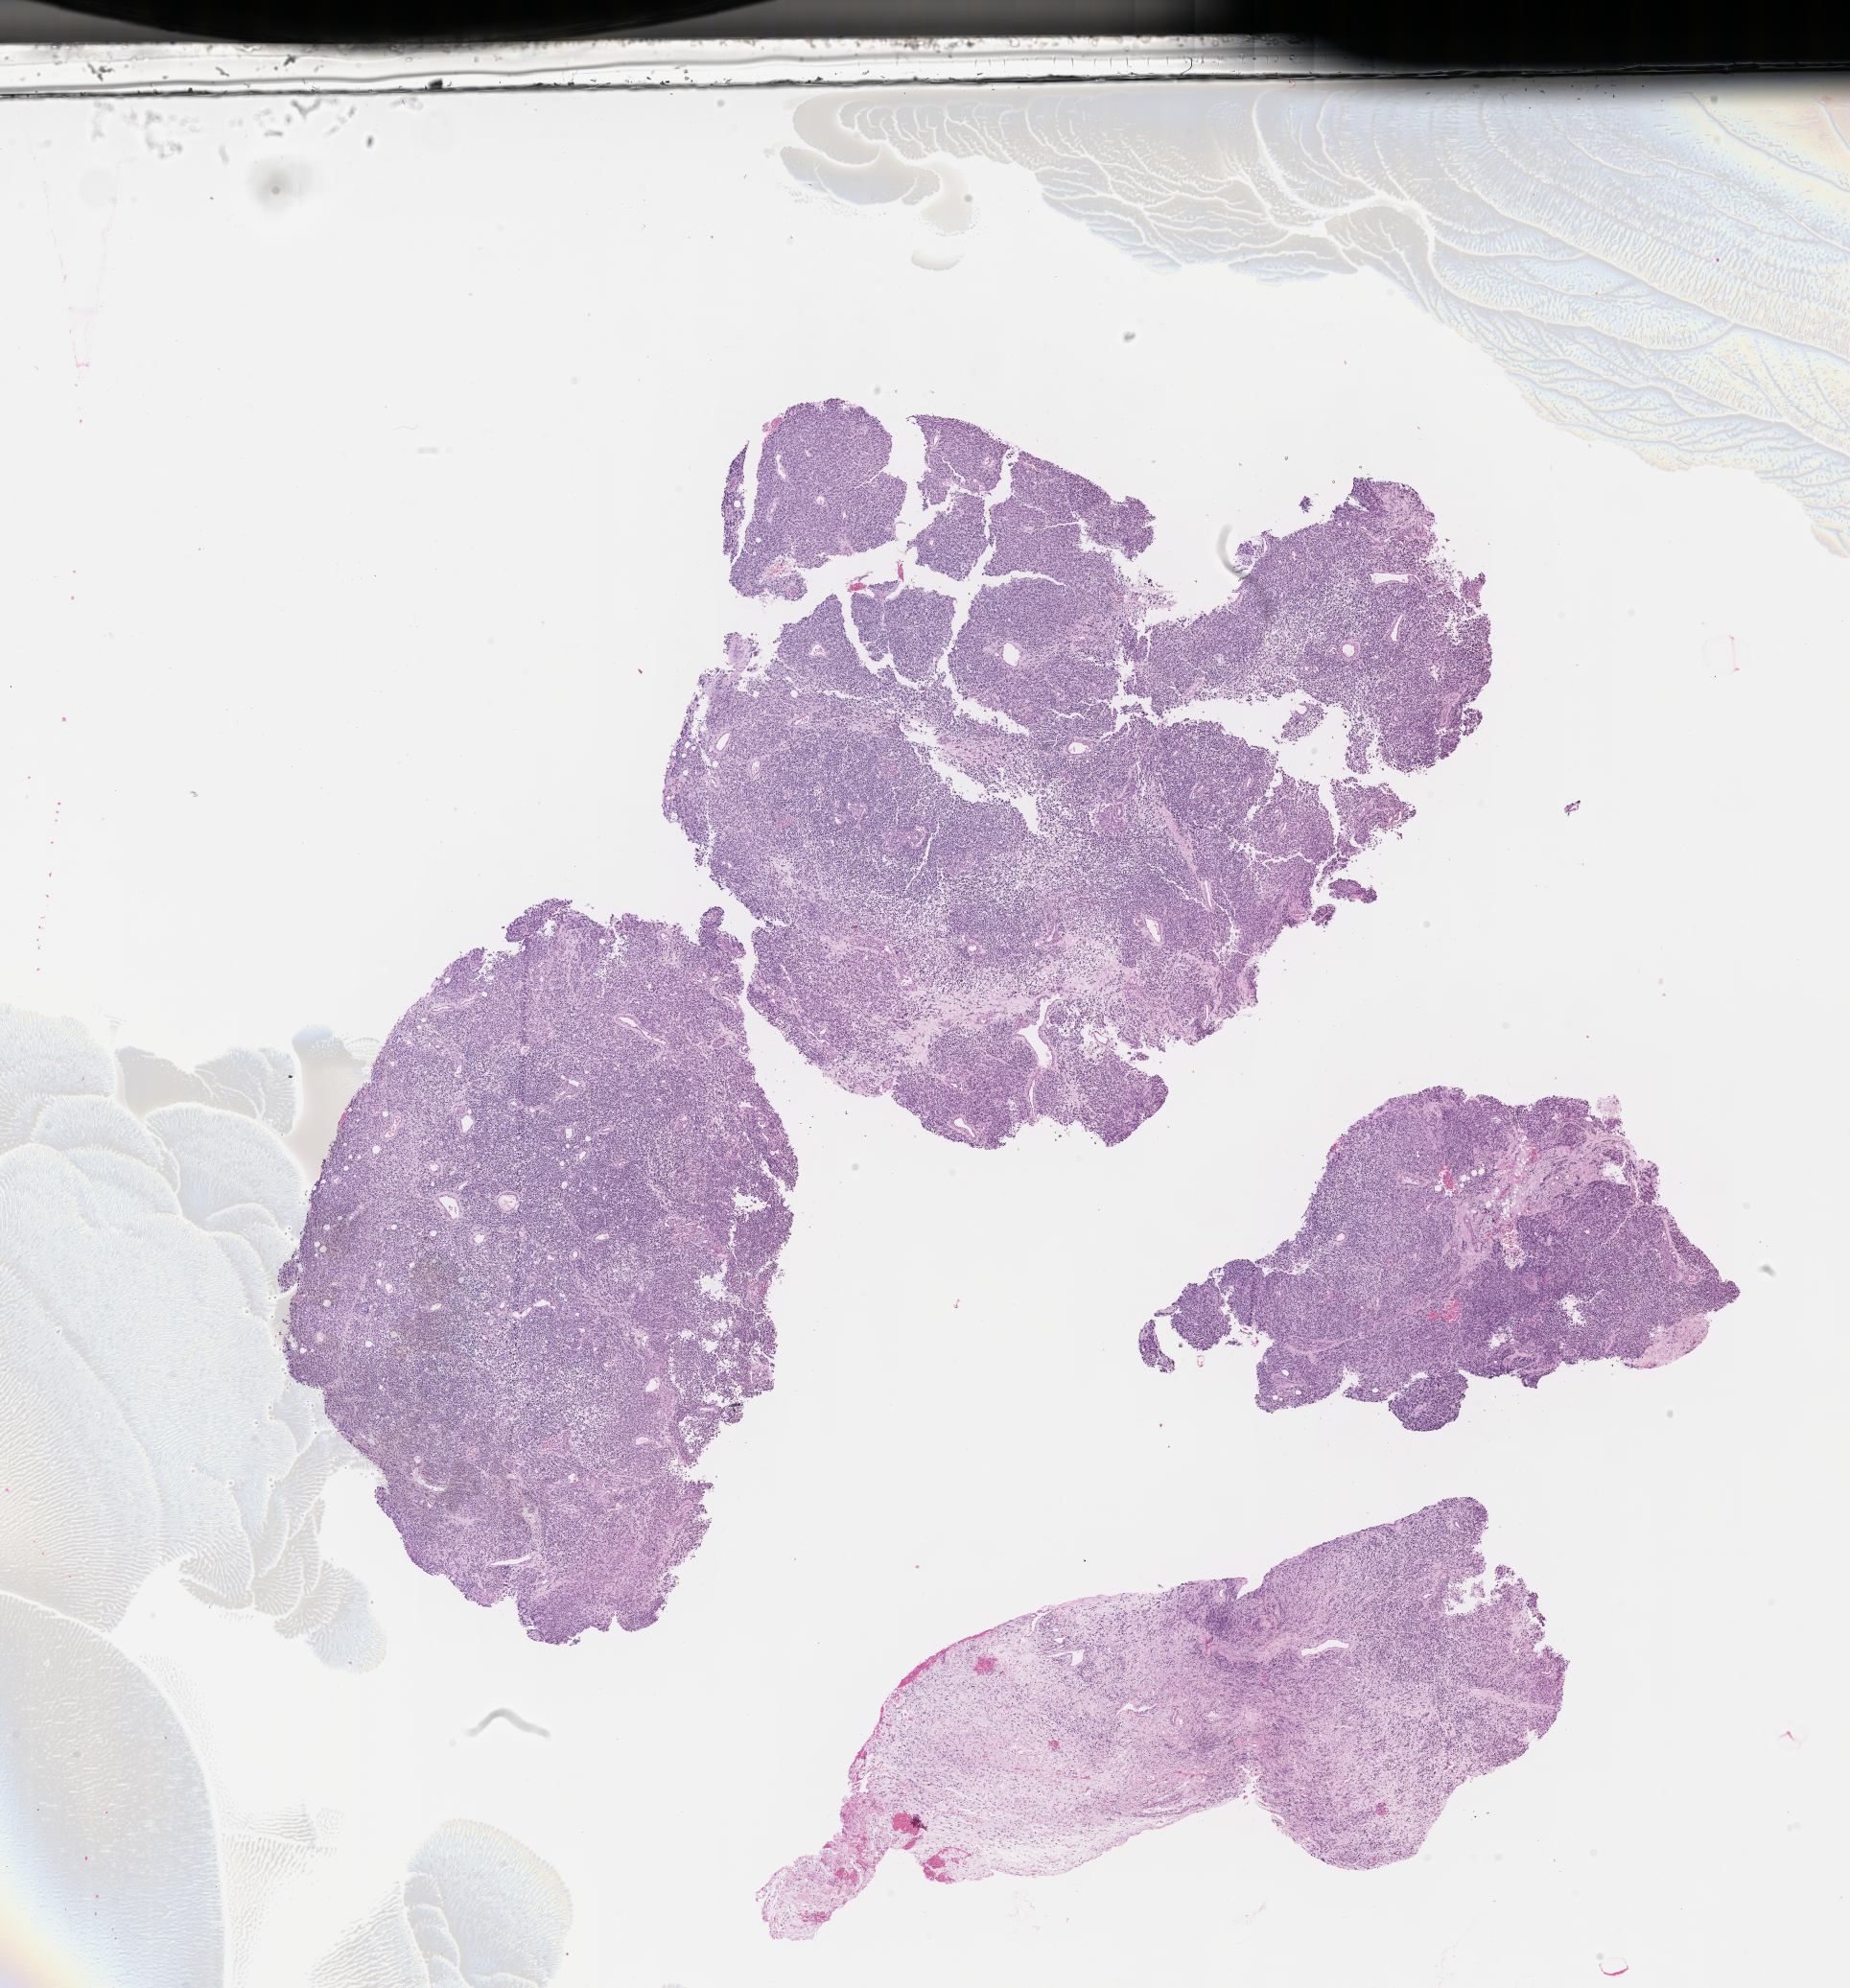
Haematoxylin and eosin whole-slide image of tumor tissue — whole scanned area (about 15.6 x 16.8 mm) shown as a low-resolution overview. FFPE section. Sample anatomic site: retroperitoneum. Female patient, age at diagnosis 8.4 years.
Metastatic status at presentation (as recorded): metastatic (confirmed). Stage (as recorded): 4. Diagnosis: rhabdomyosarcoma; histological classification: embryonal rhabdomyosarcoma.